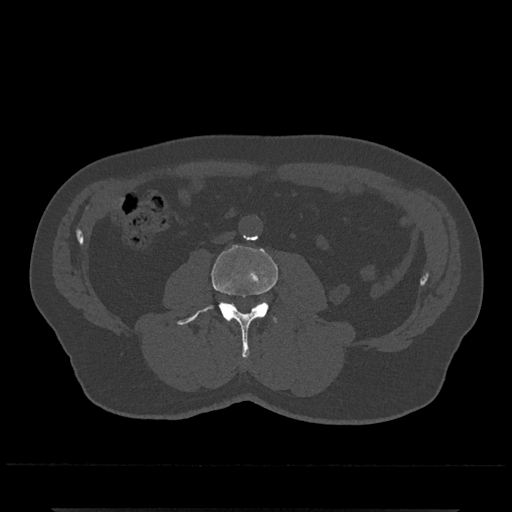
CT including the spine, one axial slice. Position 216 of 797 along the scan axis. Reconstruction kernel Br40s/3. 120 kVp. Bone window (W 1800 / L 400 HU). 0.5 mm slice thickness. 512 × 512 image matrix, field of view 393 × 393 mm. Male patient, age 67 years. From the clinical record (not read from this slice): primary cancer: prostate.
Outlined on this slice (semi-automatic segmentation, software-assisted and operator-edited):
- L3 vertebra: box from (x=177, y=245) to (x=278, y=358) px